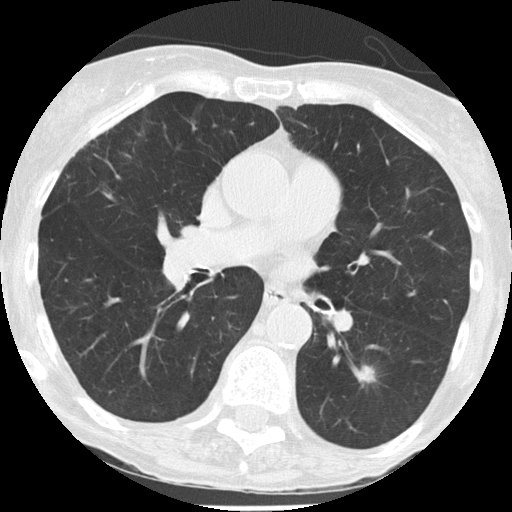
Chest CT (low-dose screening protocol), one axial image, third annual screen, lung window (W 1500 / L -600 HU), lung (sharp) reconstruction kernel (FC51), 120 kVp, 512 × 512 image matrix. Female participant, aged 68 years at enrolment.
Expert-annotated lung lesion, bounding box [x1, y1, x2, y2] px = [335, 347, 399, 405]. Screening reader's record for this exam (one nodule recorded; not confirmed to be the boxed lesion): non-calcified nodule or mass ≥4 mm, left lower lobe, 11 × 9 mm, spiculated (stellate) margins, soft tissue attenuation, pre-existing on the prior screen: yes; interval growth: yes. Official screen result: positive, other.